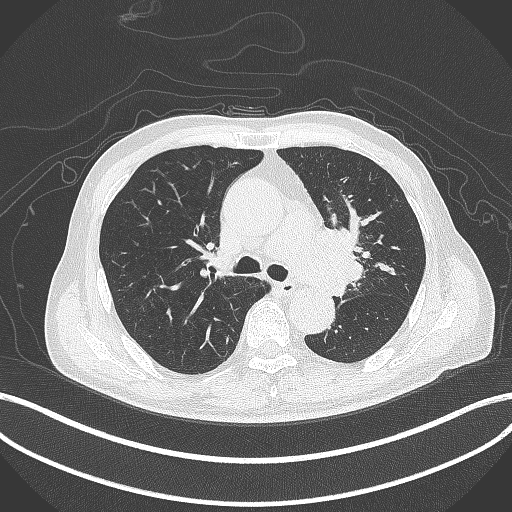
Chest CT, one axial slice; position 278 of 417 along the scan axis; reconstruction kernel B70f; 120 kVp; lung window (W 1500 / L -600 HU); 512 × 512 image matrix. Male patient, age 77 years. From the clinical record (not read from this slice): clinical TNM (as recorded): T3 N1 M0.
Structures marked on this image (bounding box drawn by a radiologist):
- lung tumour (recorded histology: adenocarcinoma): bounding box <310,224,366,297> (left, top, right, bottom; pixels)